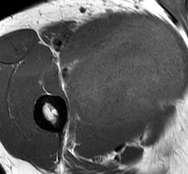
MRI of an extremity soft-tissue mass, one axial slice; slice 48 of 93 in the series (ordered by position); MR volume resampled by the dataset authors to the PET/CT grid (not the native acquisition matrix); 3.27 mm slice thickness; 188 × 174 image matrix, field of view 184 × 170 mm. Male patient. Case-level facts recorded for this patient, not image findings: histological type: undifferentiated - pleiomorphic; grade: high; site of the primary tumour: right thigh.
Outlined on this slice (expert contour drawn on MRI and transferred to this co-registered scan by the dataset authors):
- gross tumour volume including surrounding oedema: bounding box <66,17,185,130> (left, top, right, bottom; pixels)
- gross tumour volume (mass): <74,17,185,129>